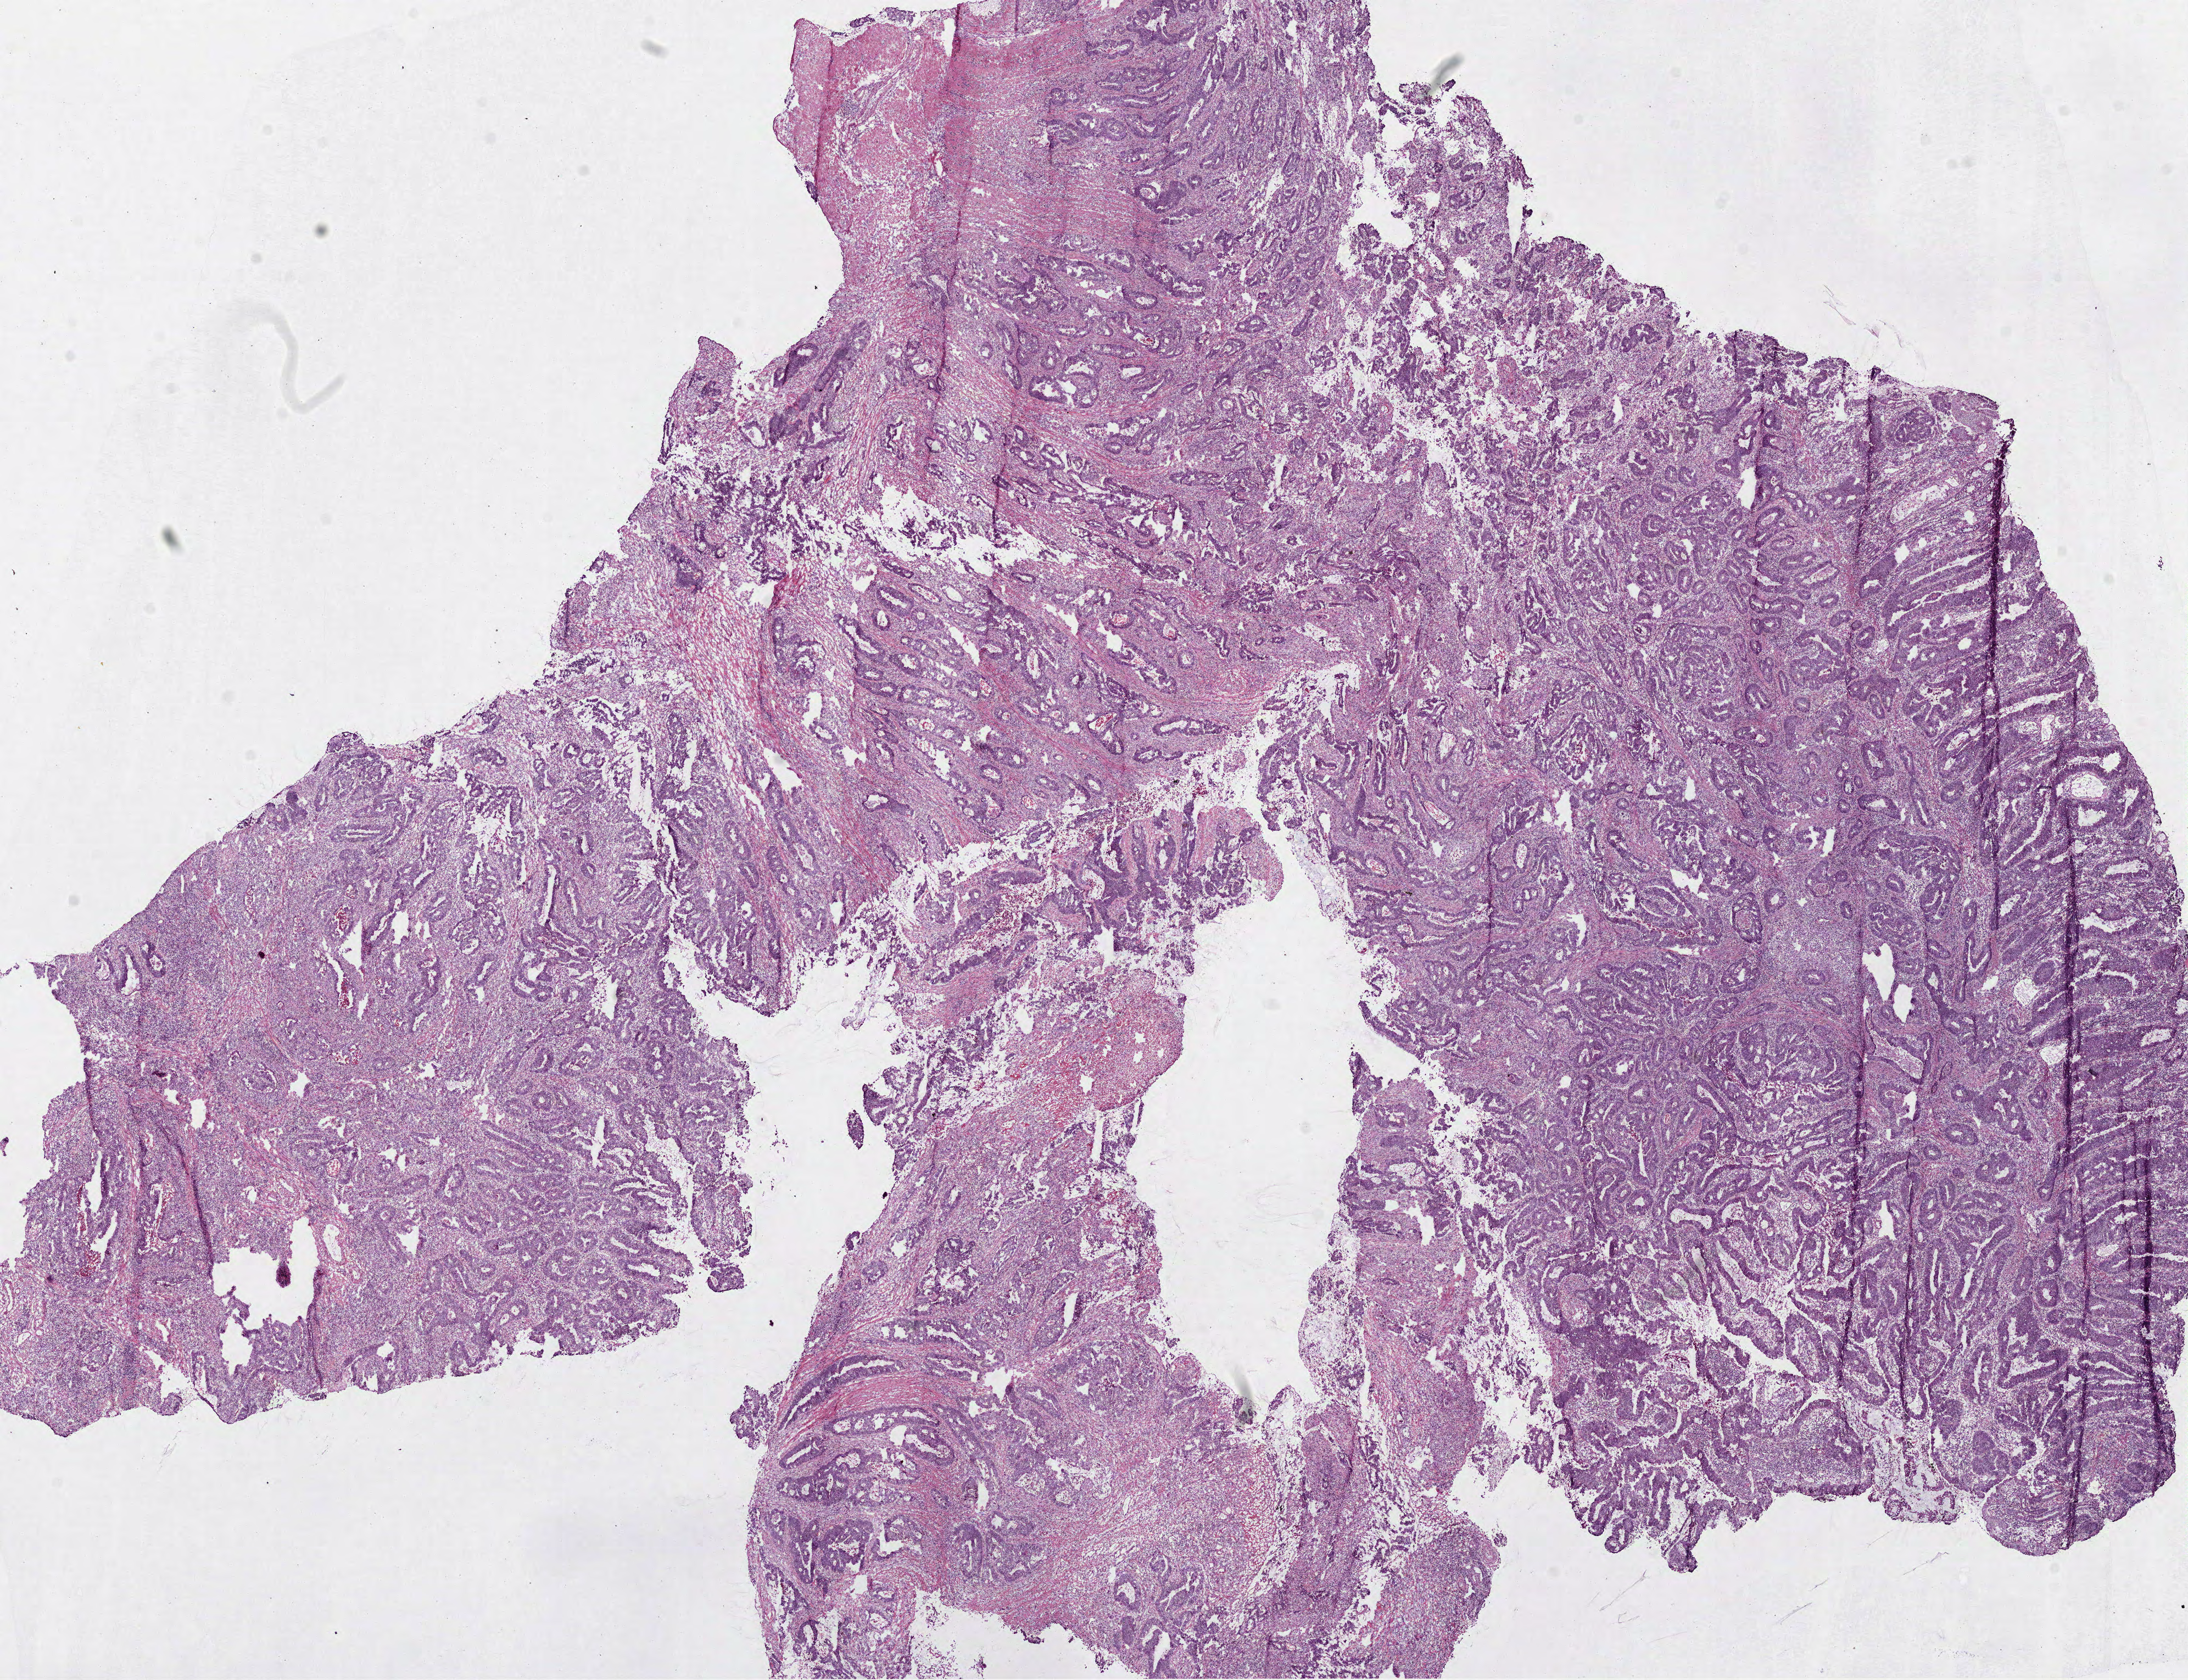
Hematoxylin and eosin (H&E) stained whole-slide image, shown as a low-resolution overview of the whole scanned area (about 16.1 x 12.3 mm, slide scanned at 40x); frozen section from the bottom of the tissue portion; sample: primary tumour, colon. Patient: female, age at initial diagnosis 75 years. Composition of this section per pathologist review: tumour cells 70%, tumour nuclei 60%, normal cells 0%, stromal cells 20%, necrosis 10%.
• lymph nodes positive (case pathology): 0 of 20 examined
• pathologic diagnosis: Adenocarcinoma, NOS (hepatic flexure of colon)
• AJCC pathologic stage: IIA (7th edition)